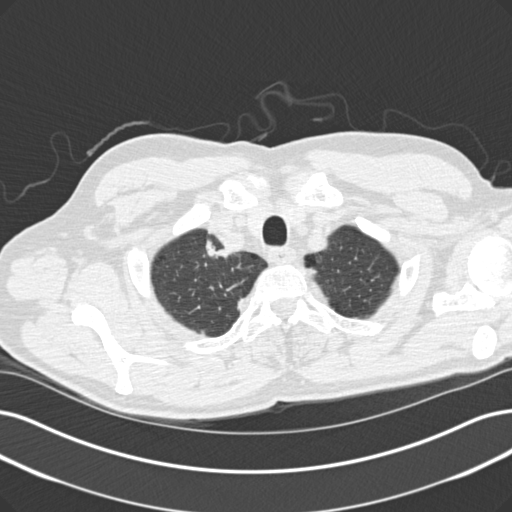
Low-dose screening chest CT, one axial slice; position 132 of 152 along the scan axis; reconstruction kernel B30f; lung window (W 1500 / L -600 HU); 2 mm slice thickness; 512 × 512 image matrix.
Annotated regions visible in this slice (expert manual segmentation):
- lesion 1 (tumor, upper lobe of right lung): bounding box (x1, y1, x2, y2) in pixels: (206, 240, 227, 258)